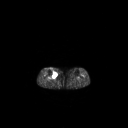
FDG PET of an extremity soft-tissue mass (from a PET/CT study), one axial slice; position 148 of 267 along the scan axis; 128 × 128 image matrix, field of view 700 × 700 mm. Female patient, age 65 years. Case-level facts recorded for this patient, not image findings: histological type: undifferentiated – high grade; grade: high; site of the primary tumour: right thigh.
Structures marked on this image (expert contour drawn on MRI and transferred to this co-registered scan by the dataset authors):
- gross tumour volume (mass): bounding box (x1, y1, x2, y2) in pixels: (51, 71, 57, 78)